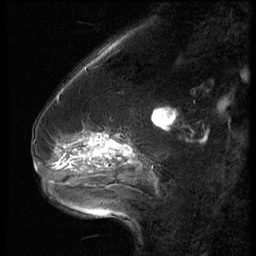
Breast MRI (dynamic contrast-enhanced), one sagittal slice; slice 20 of 62 in the series (ordered by position); 3 images stored at this slice position (order not interpretable as contrast timing); 1.5 T; TE 4.2 ms, TR 9 ms; 2.5 mm slice thickness; 256 × 256 image matrix, field of view 180 × 180 mm. Female patient, age 54 years. From the clinical record (not read from this slice): setting: breast cancer imaged before/during neoadjuvant chemotherapy; receptor status: HR-positive, HER2-negative.
Structures marked on this image (semi-automatically segmented with operator editing):
- analysis volume of interest (the breast-tissue region the enhancement analysis was run in; not a lesion): bounding box (x1, y1, x2, y2) in pixels: (42, 126, 146, 183)
- tumour enhancement mask (voxels above the 140 % enhancement threshold inside the analysis volume of interest): (84, 134, 127, 159)